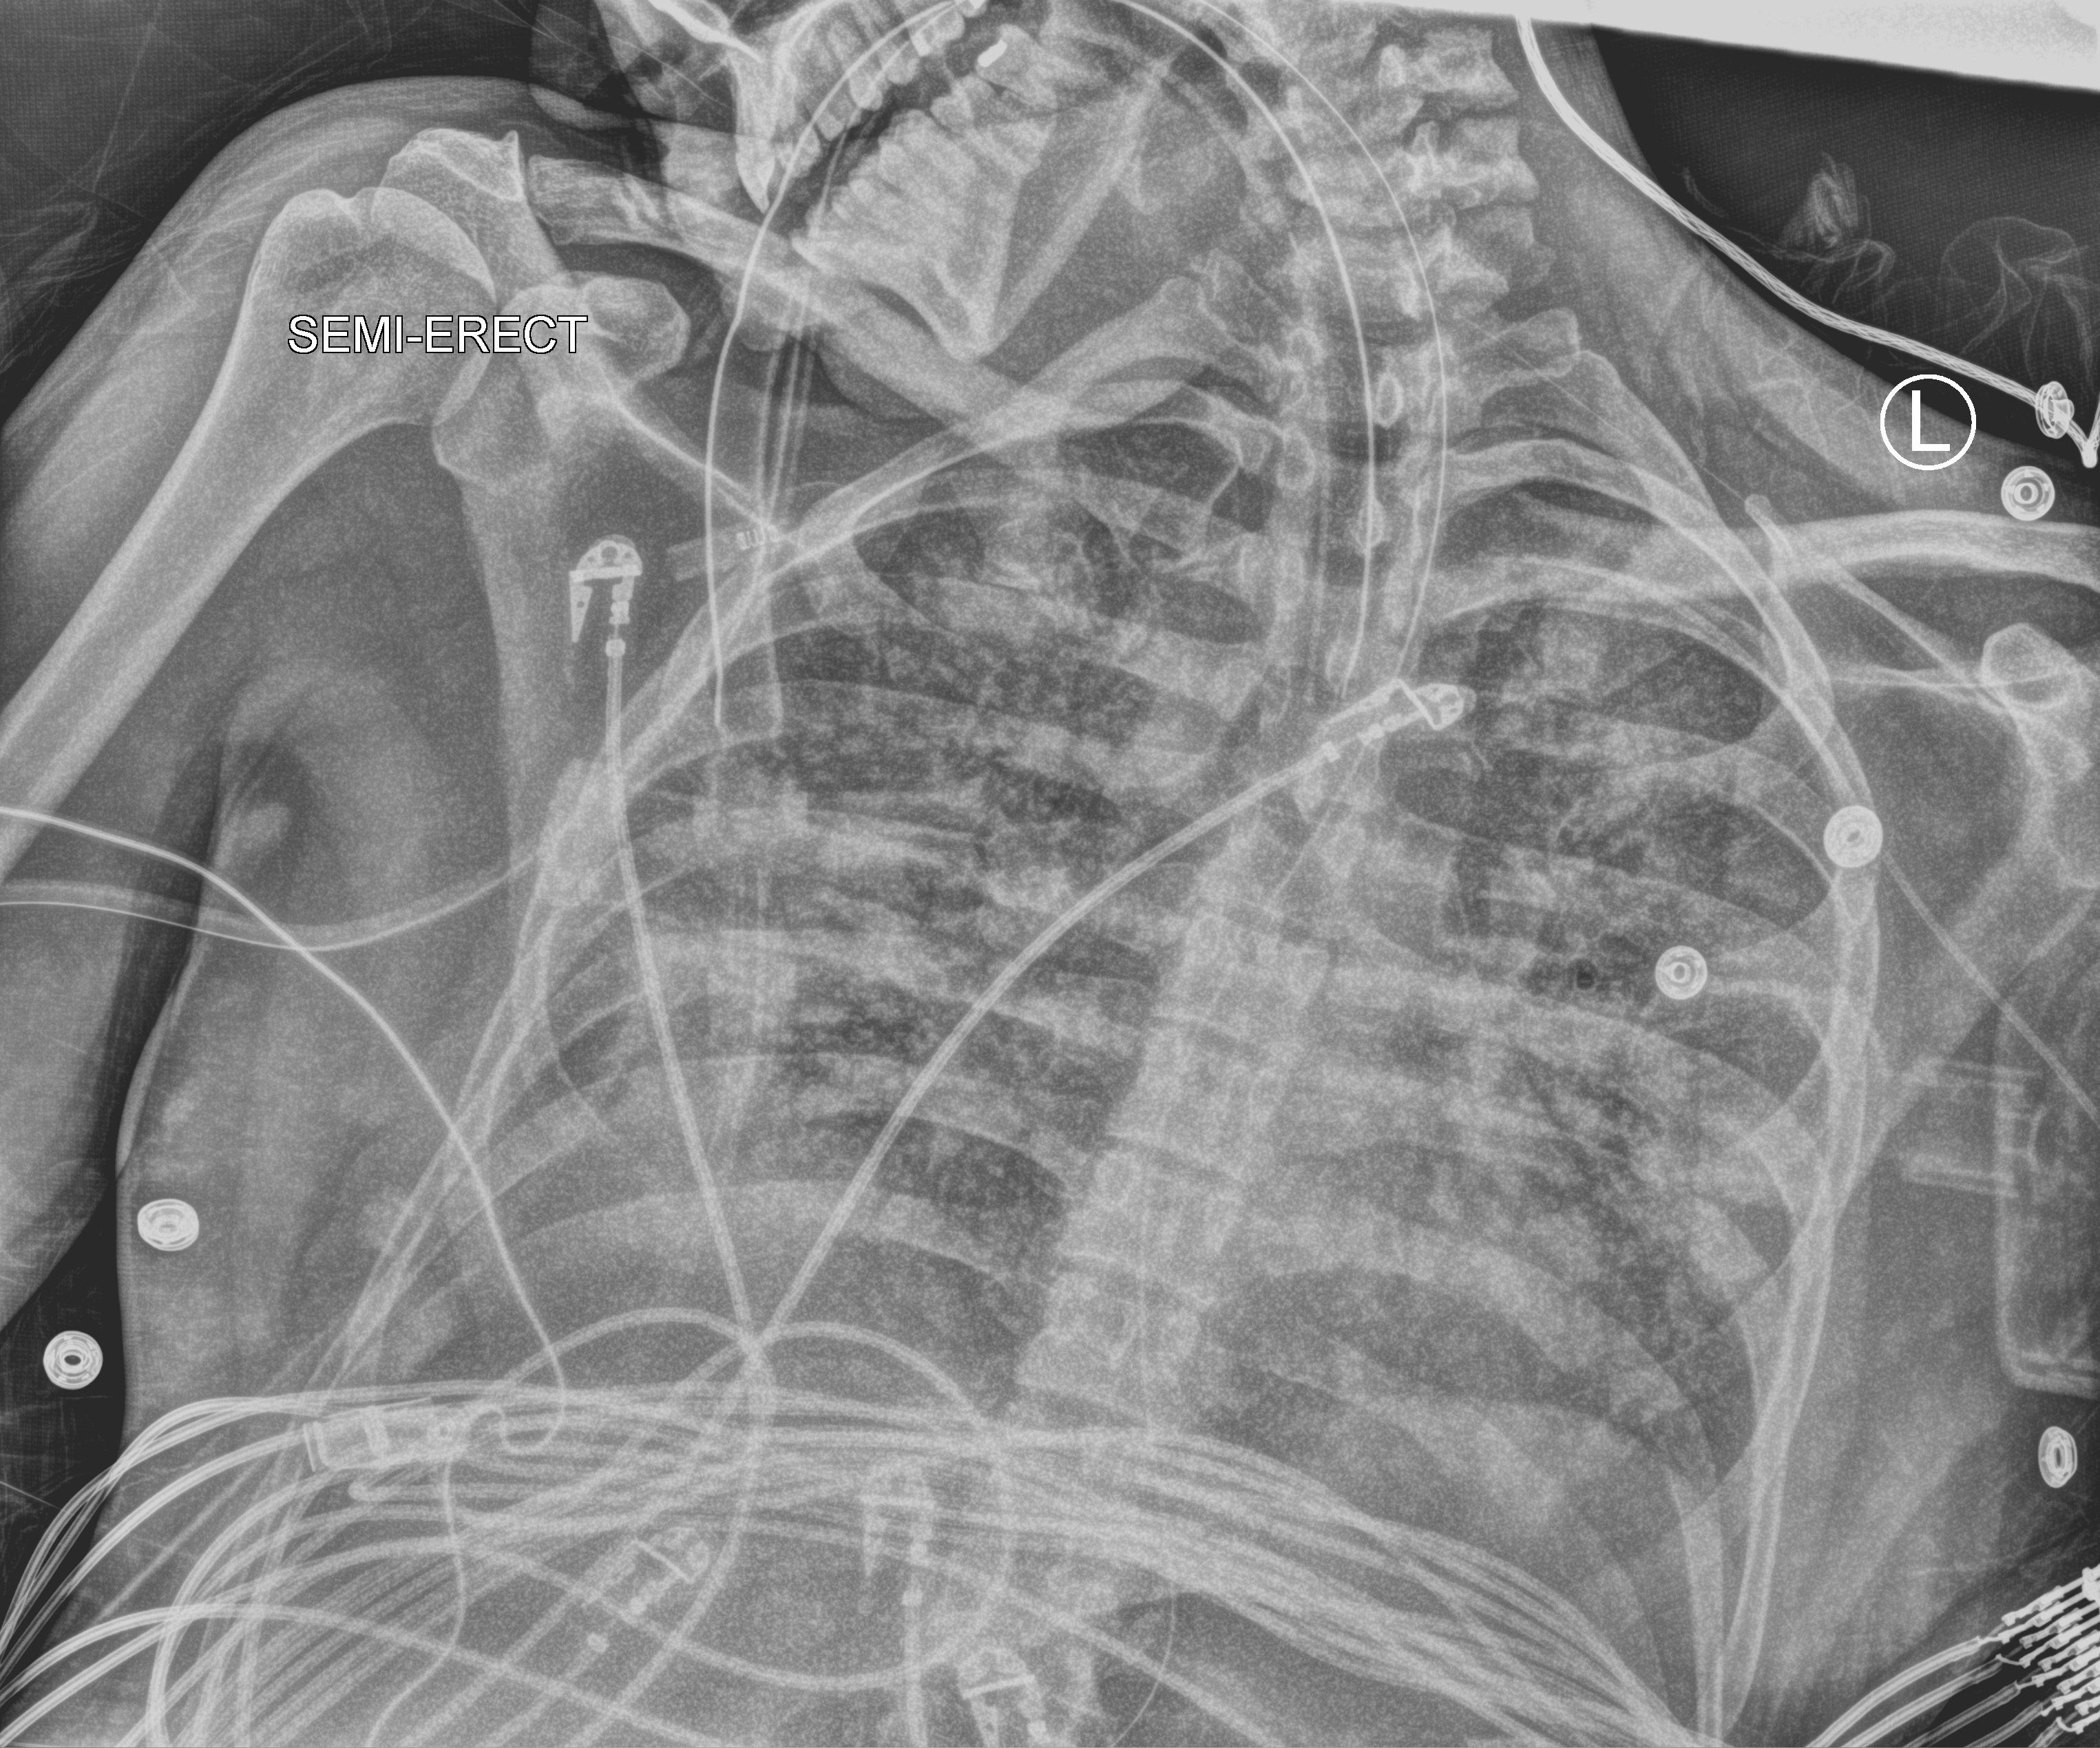
Bedside chest radiograph (computed radiography). Male patient hospitalised with COVID-19, age 18–59 years.
Admission-level facts for this patient (not findings on this image; timing relative to this image not recorded): diabetes (admission record): no; hypertension (admission record): no; admitted to intensive care during this hospital stay: yes.